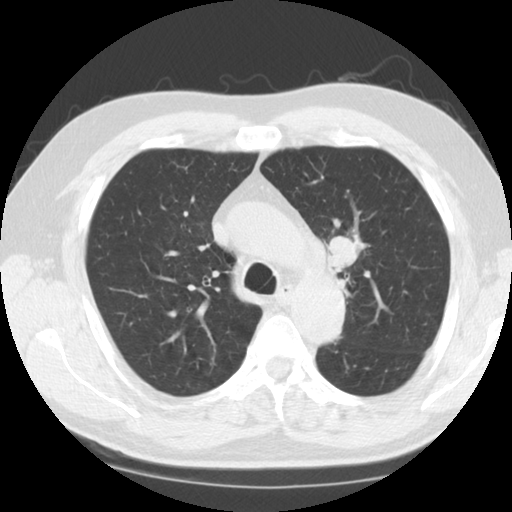
Axial slice from a low-dose chest CT screening exam. Third screening round (two years after baseline). Lung window (W 1500 / L -600 HU). Standard (soft-tissue) reconstruction kernel (STANDARD). Slice 35 of 124 in the series. Male participant, aged 60 years at enrolment.
Expert reader's lesion annotation, bounding box [x1, y1, x2, y2] px = [317, 224, 370, 280]. Screening reader's record for this exam (one nodule recorded; not confirmed to be the boxed lesion): non-calcified nodule or mass ≥4 mm, left upper lobe, 24 × 21 mm, smooth margins, soft tissue attenuation, pre-existing on the prior screen: no. Official screen result: positive, other. Later outcome: lung cancer diagnosed 14 days after this screen — small cell carcinoma, NOS, left upper lobe, stage IIA (AJCC 6th edition), 26 mm at pathology.